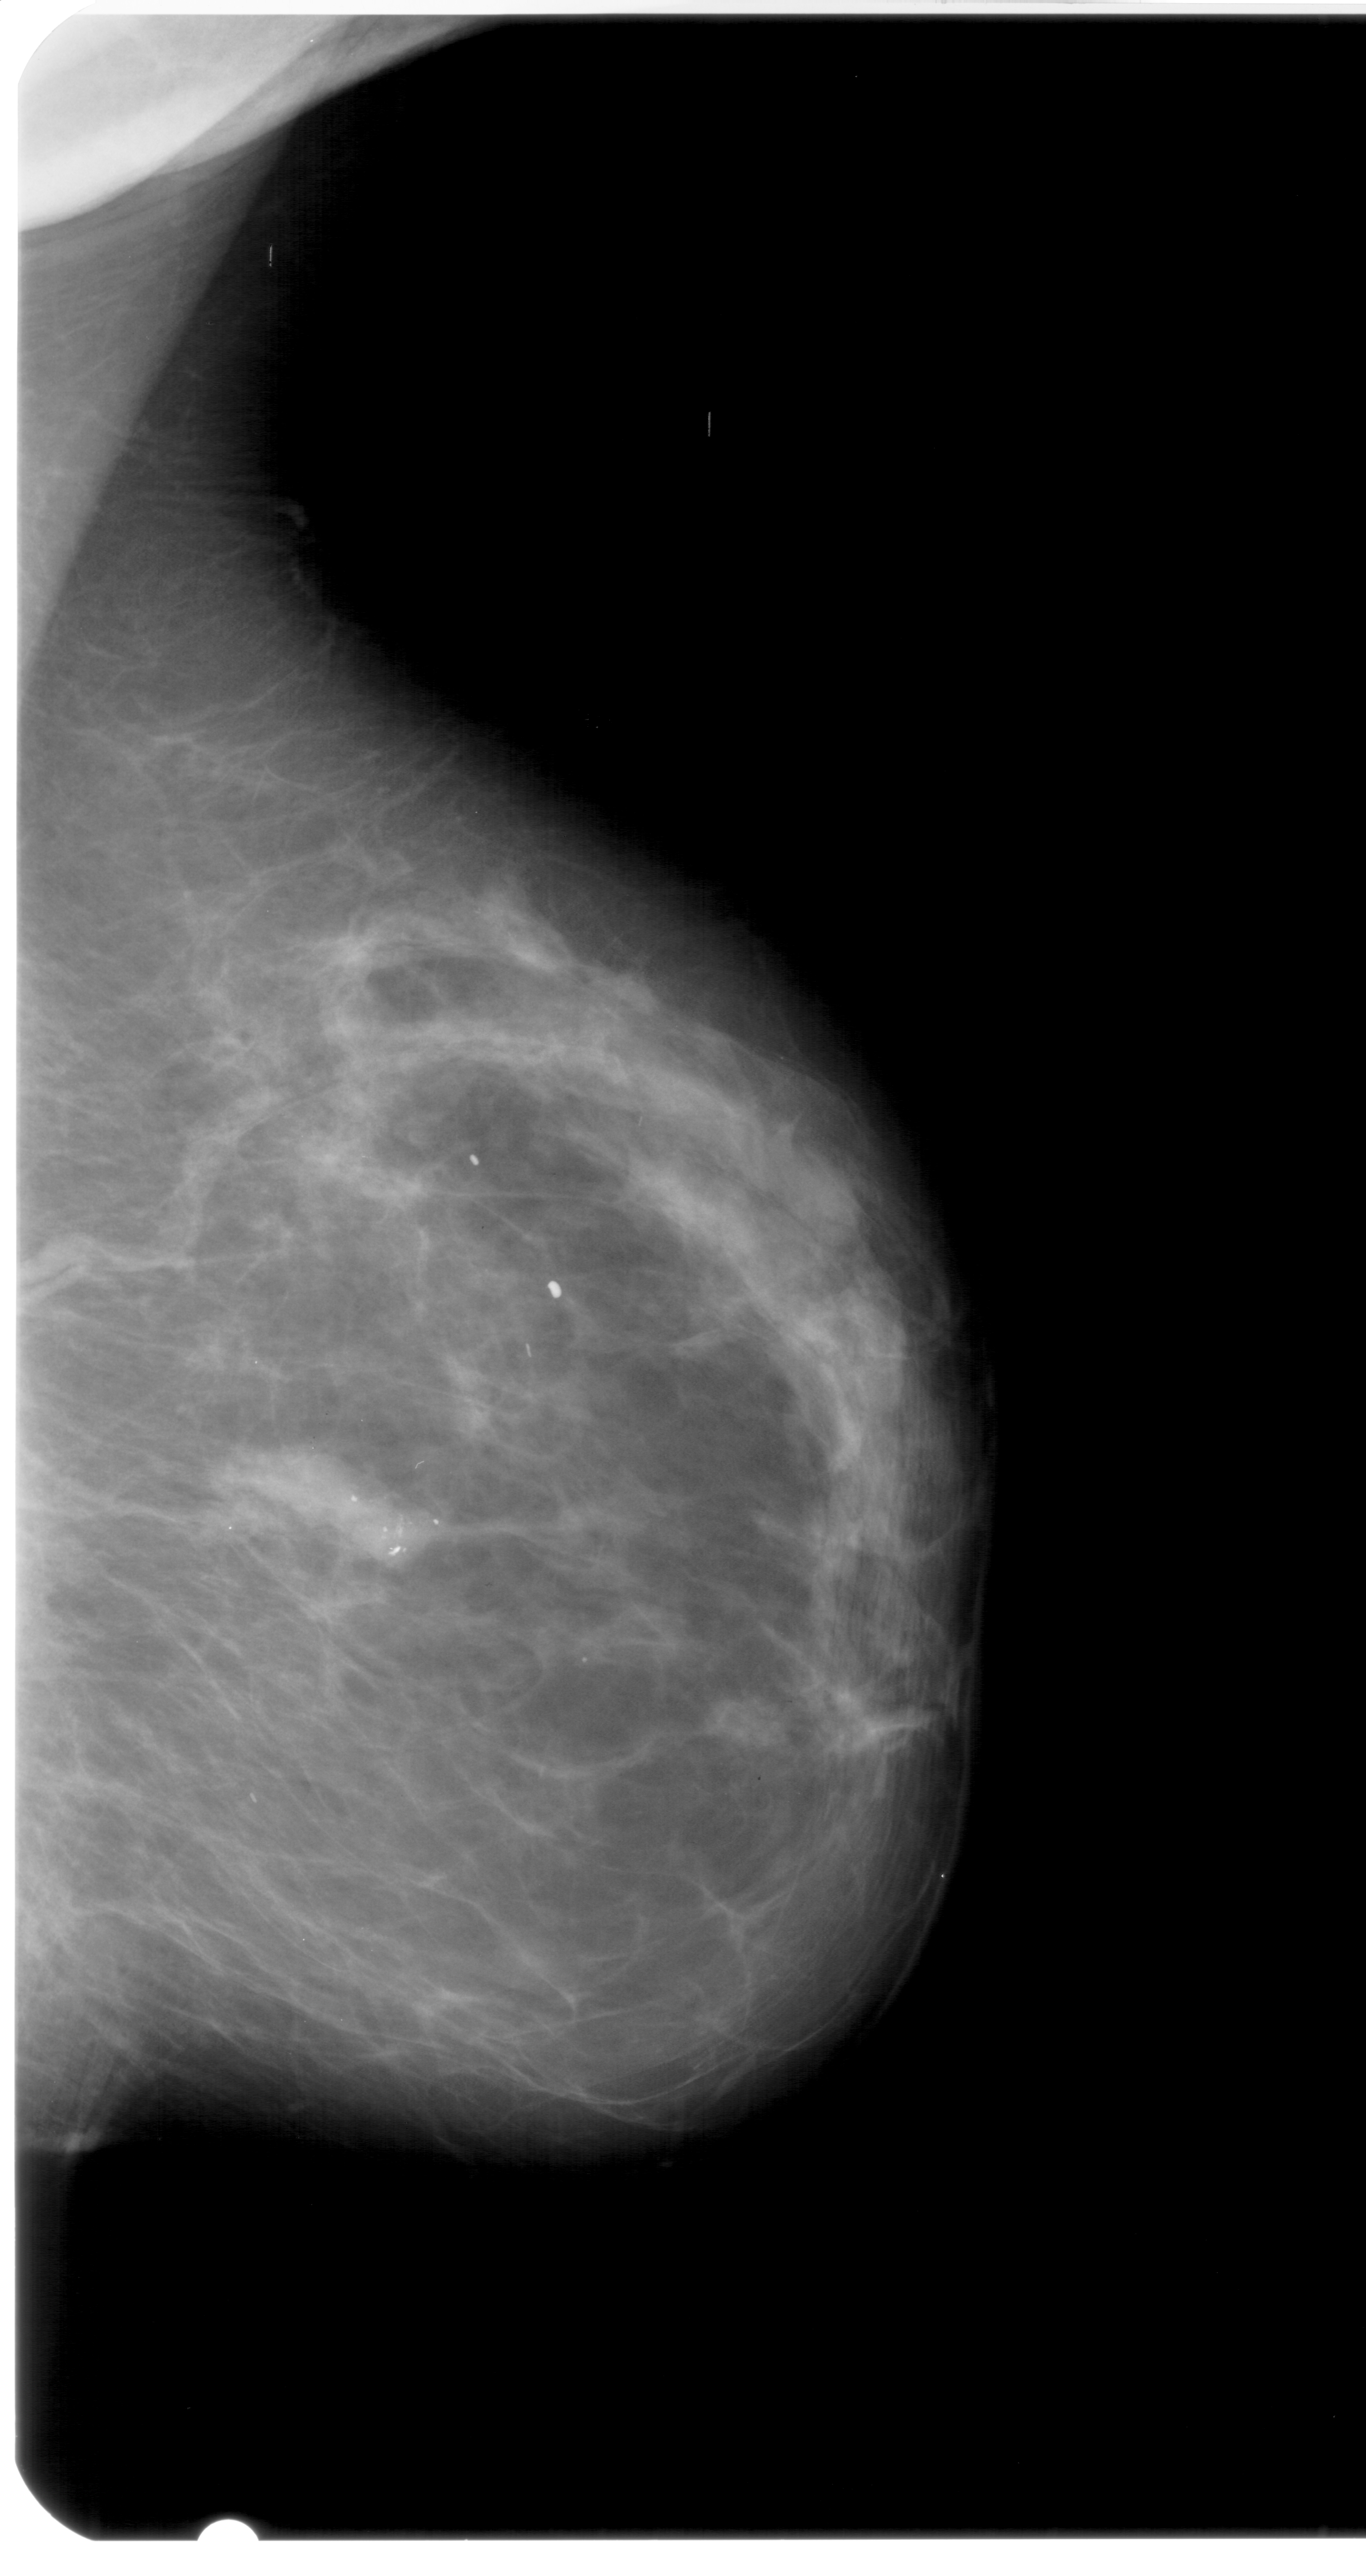
Digitized screen-film mammogram; right breast; mediolateral oblique (MLO) view; BI-RADS breast density category 2 (scale 1–4).
- Calcifications, morphology pleomorphic, distribution clustered; BI-RADS assessment category 4; subtlety rating 5 on a 1 (subtle) to 5 (obvious) scale; pathology (as recorded): malignant.